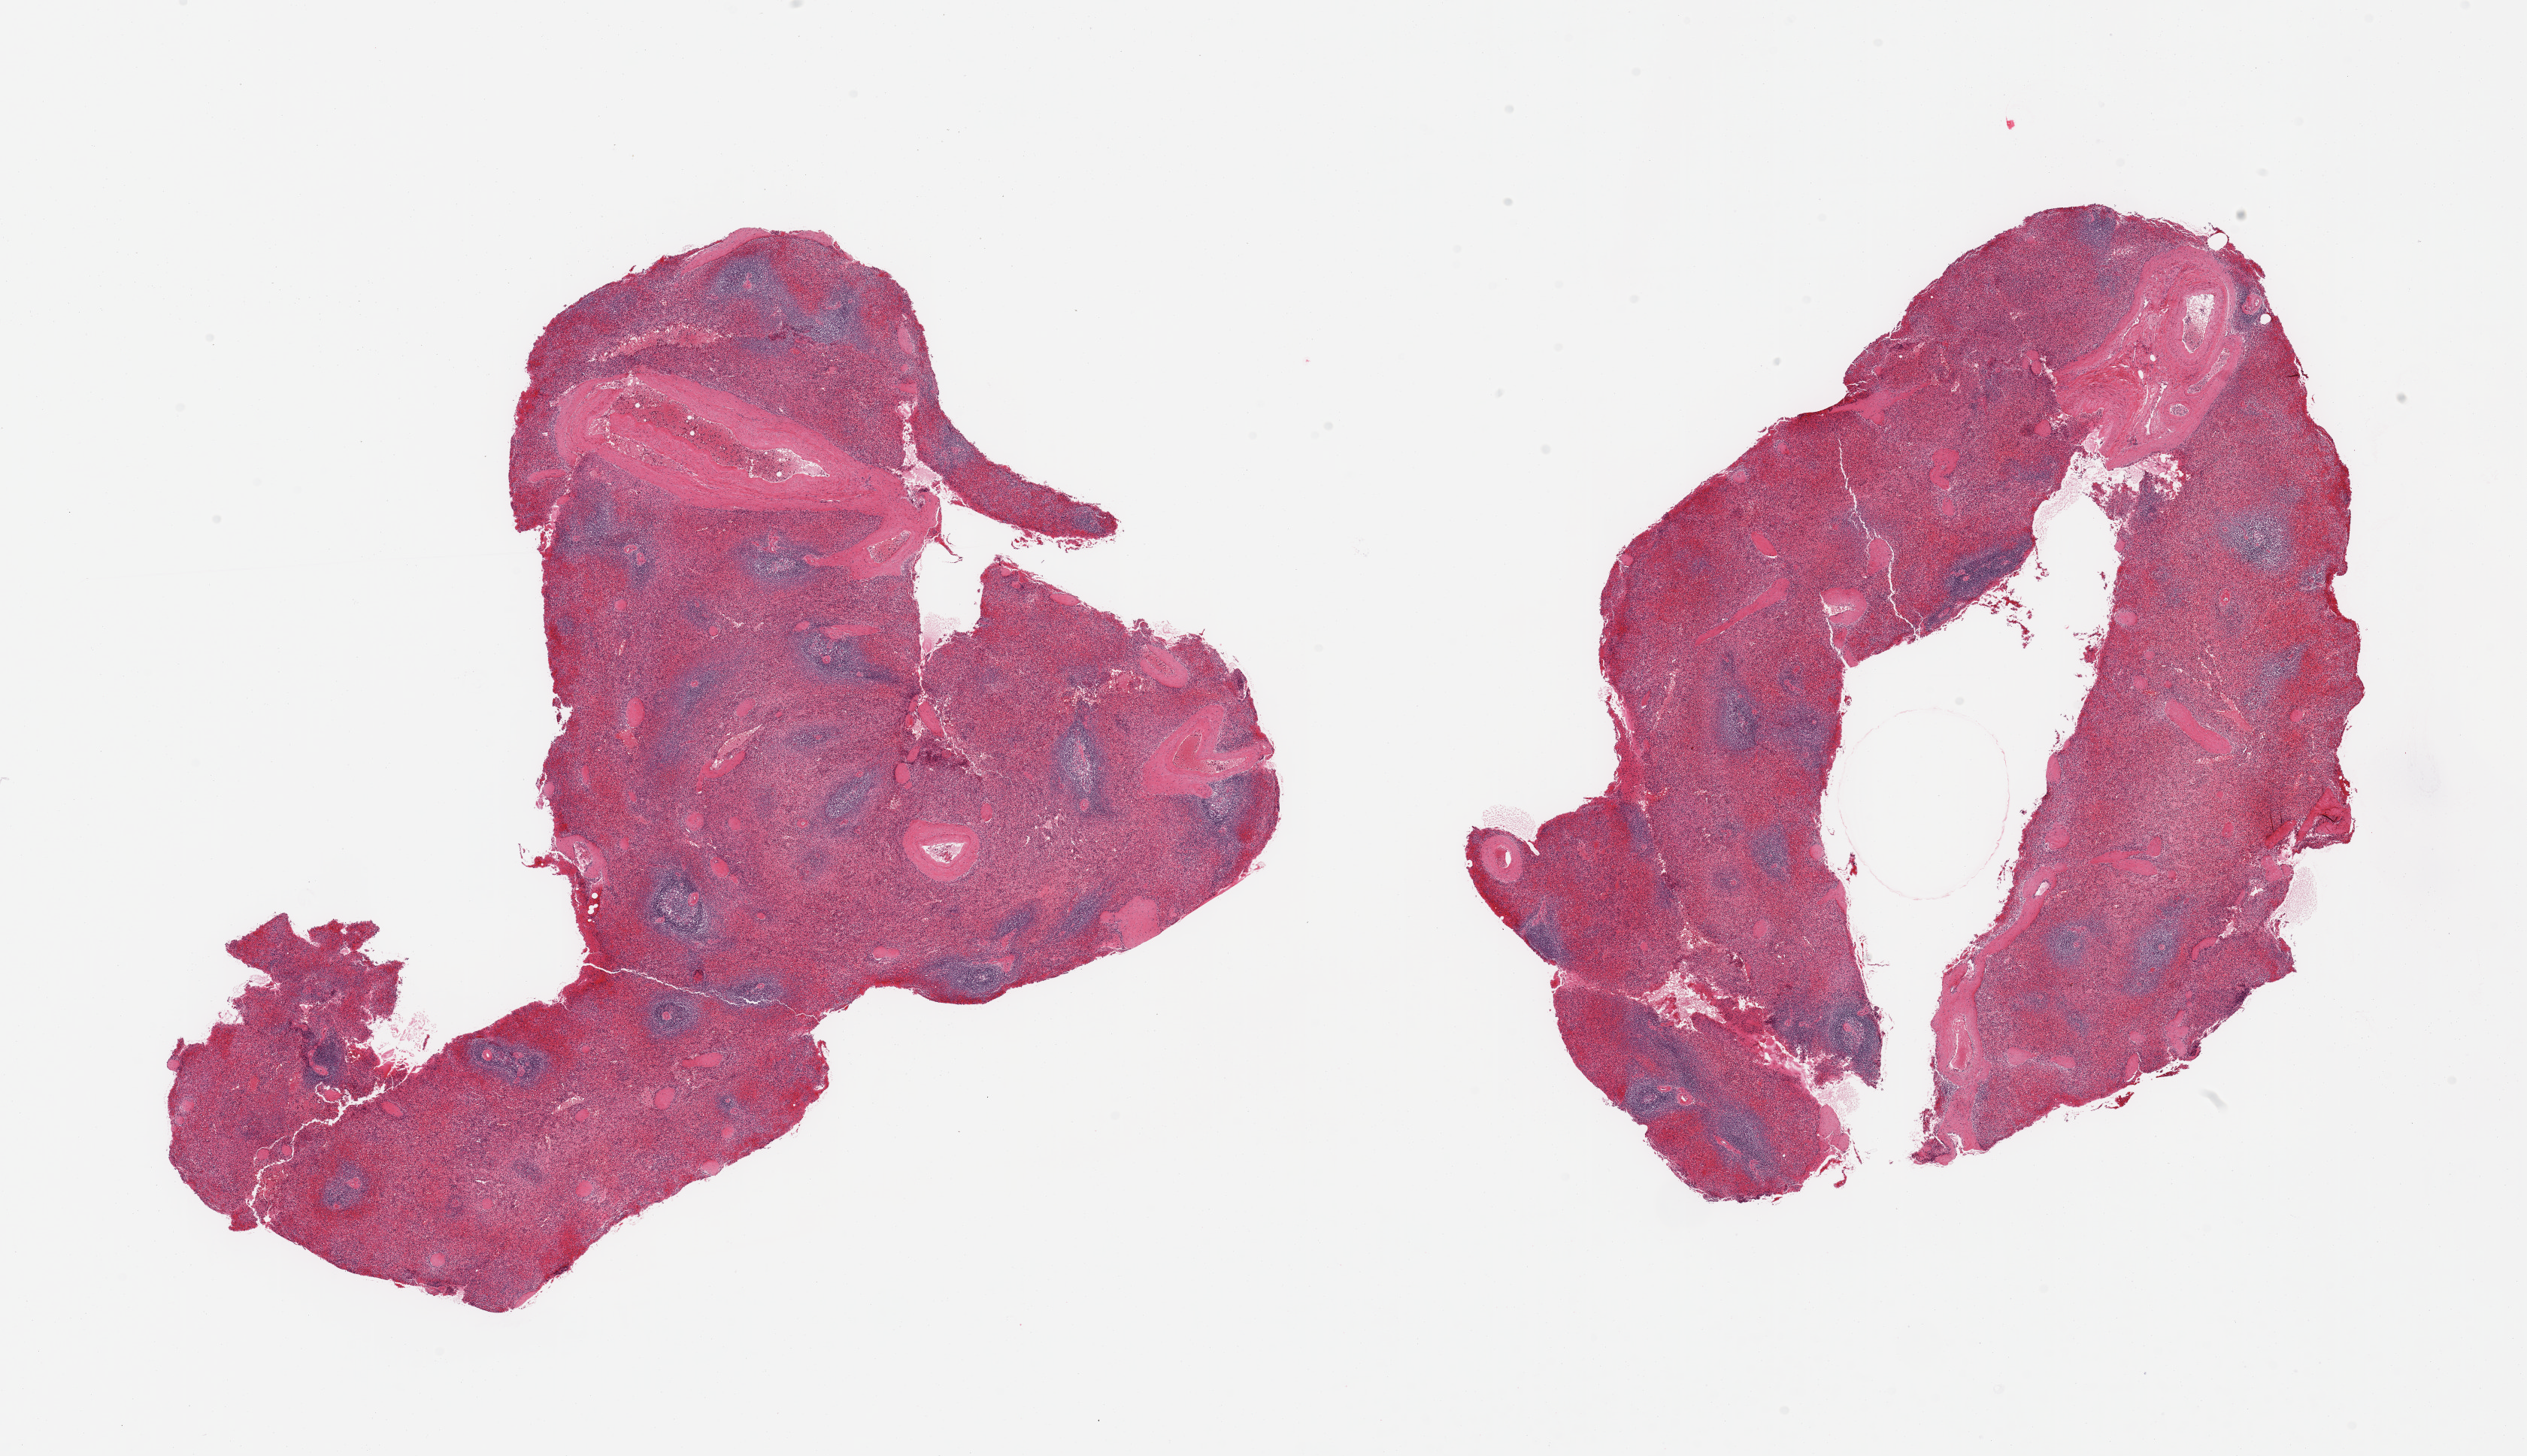
Digitized hematoxylin and eosin (H&E)-stained section, brightfield, a low-resolution overview of the entire scanned area, about 26.6 x 15.3 mm (slide scanned at 20x), PAXgene-fixed paraffin-embedded (PFPE) section, sampled site (target tissue): spleen, donor tissue sample.
Review note (as recorded): 2 pieces, advanced autolysis/congestion.